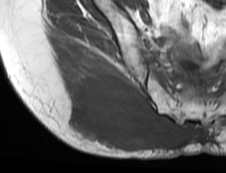
MRI of an extremity soft-tissue mass, one axial slice; slice 44 of 73 in the series (ordered by position); MR volume resampled by the dataset authors to the PET/CT grid (not the native acquisition matrix); 3.27 mm slice thickness; 226 × 173 image matrix, field of view 221 × 169 mm. Female patient. From the clinical record (not read from this slice): histological type: spindle cell suggestive of myxofibrosarcoma; grade: intermediate; site of the primary tumour: right buttock.
Structures marked on this image (expert contour drawn on MRI and transferred to this co-registered scan by the dataset authors):
- gross tumour volume (mass): bounding box <65,74,190,151> (left, top, right, bottom; pixels)